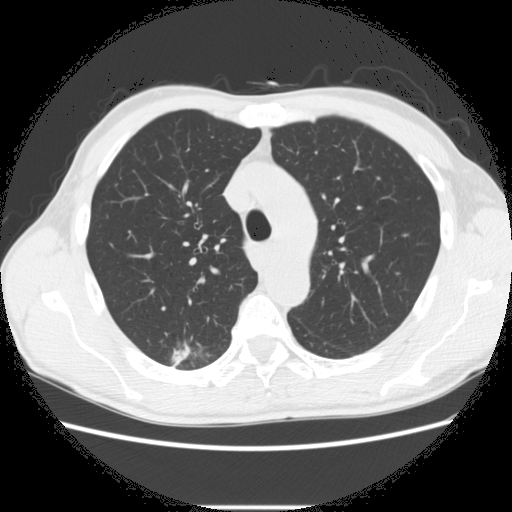
Chest CT (low-dose screening protocol), one axial image. Second annual screen. Lung window (W 1500 / L -600 HU). 2.5 mm slice thickness. 120 kVp. Slice 78 of 282 in the series. 512 × 512 image matrix. Male, age 66 years at enrolment. Former smoker at enrolment.
Lesion marked by an expert reader, bounding box [x1, y1, x2, y2] px = [162, 338, 222, 375]. The screening reader recorded 5 non-calcified nodules or masses ≥4 mm on this exam (right lower lobe, right upper lobe, right upper lobe, right upper lobe, left lower lobe); which of them this box marks is not recorded. Participant outcome: lung cancer diagnosed 75 days after this screen — adenocarcinoma, NOS, right upper lobe, undifferentiated (G4), stage IA (AJCC 6th edition), 20 mm at pathology.